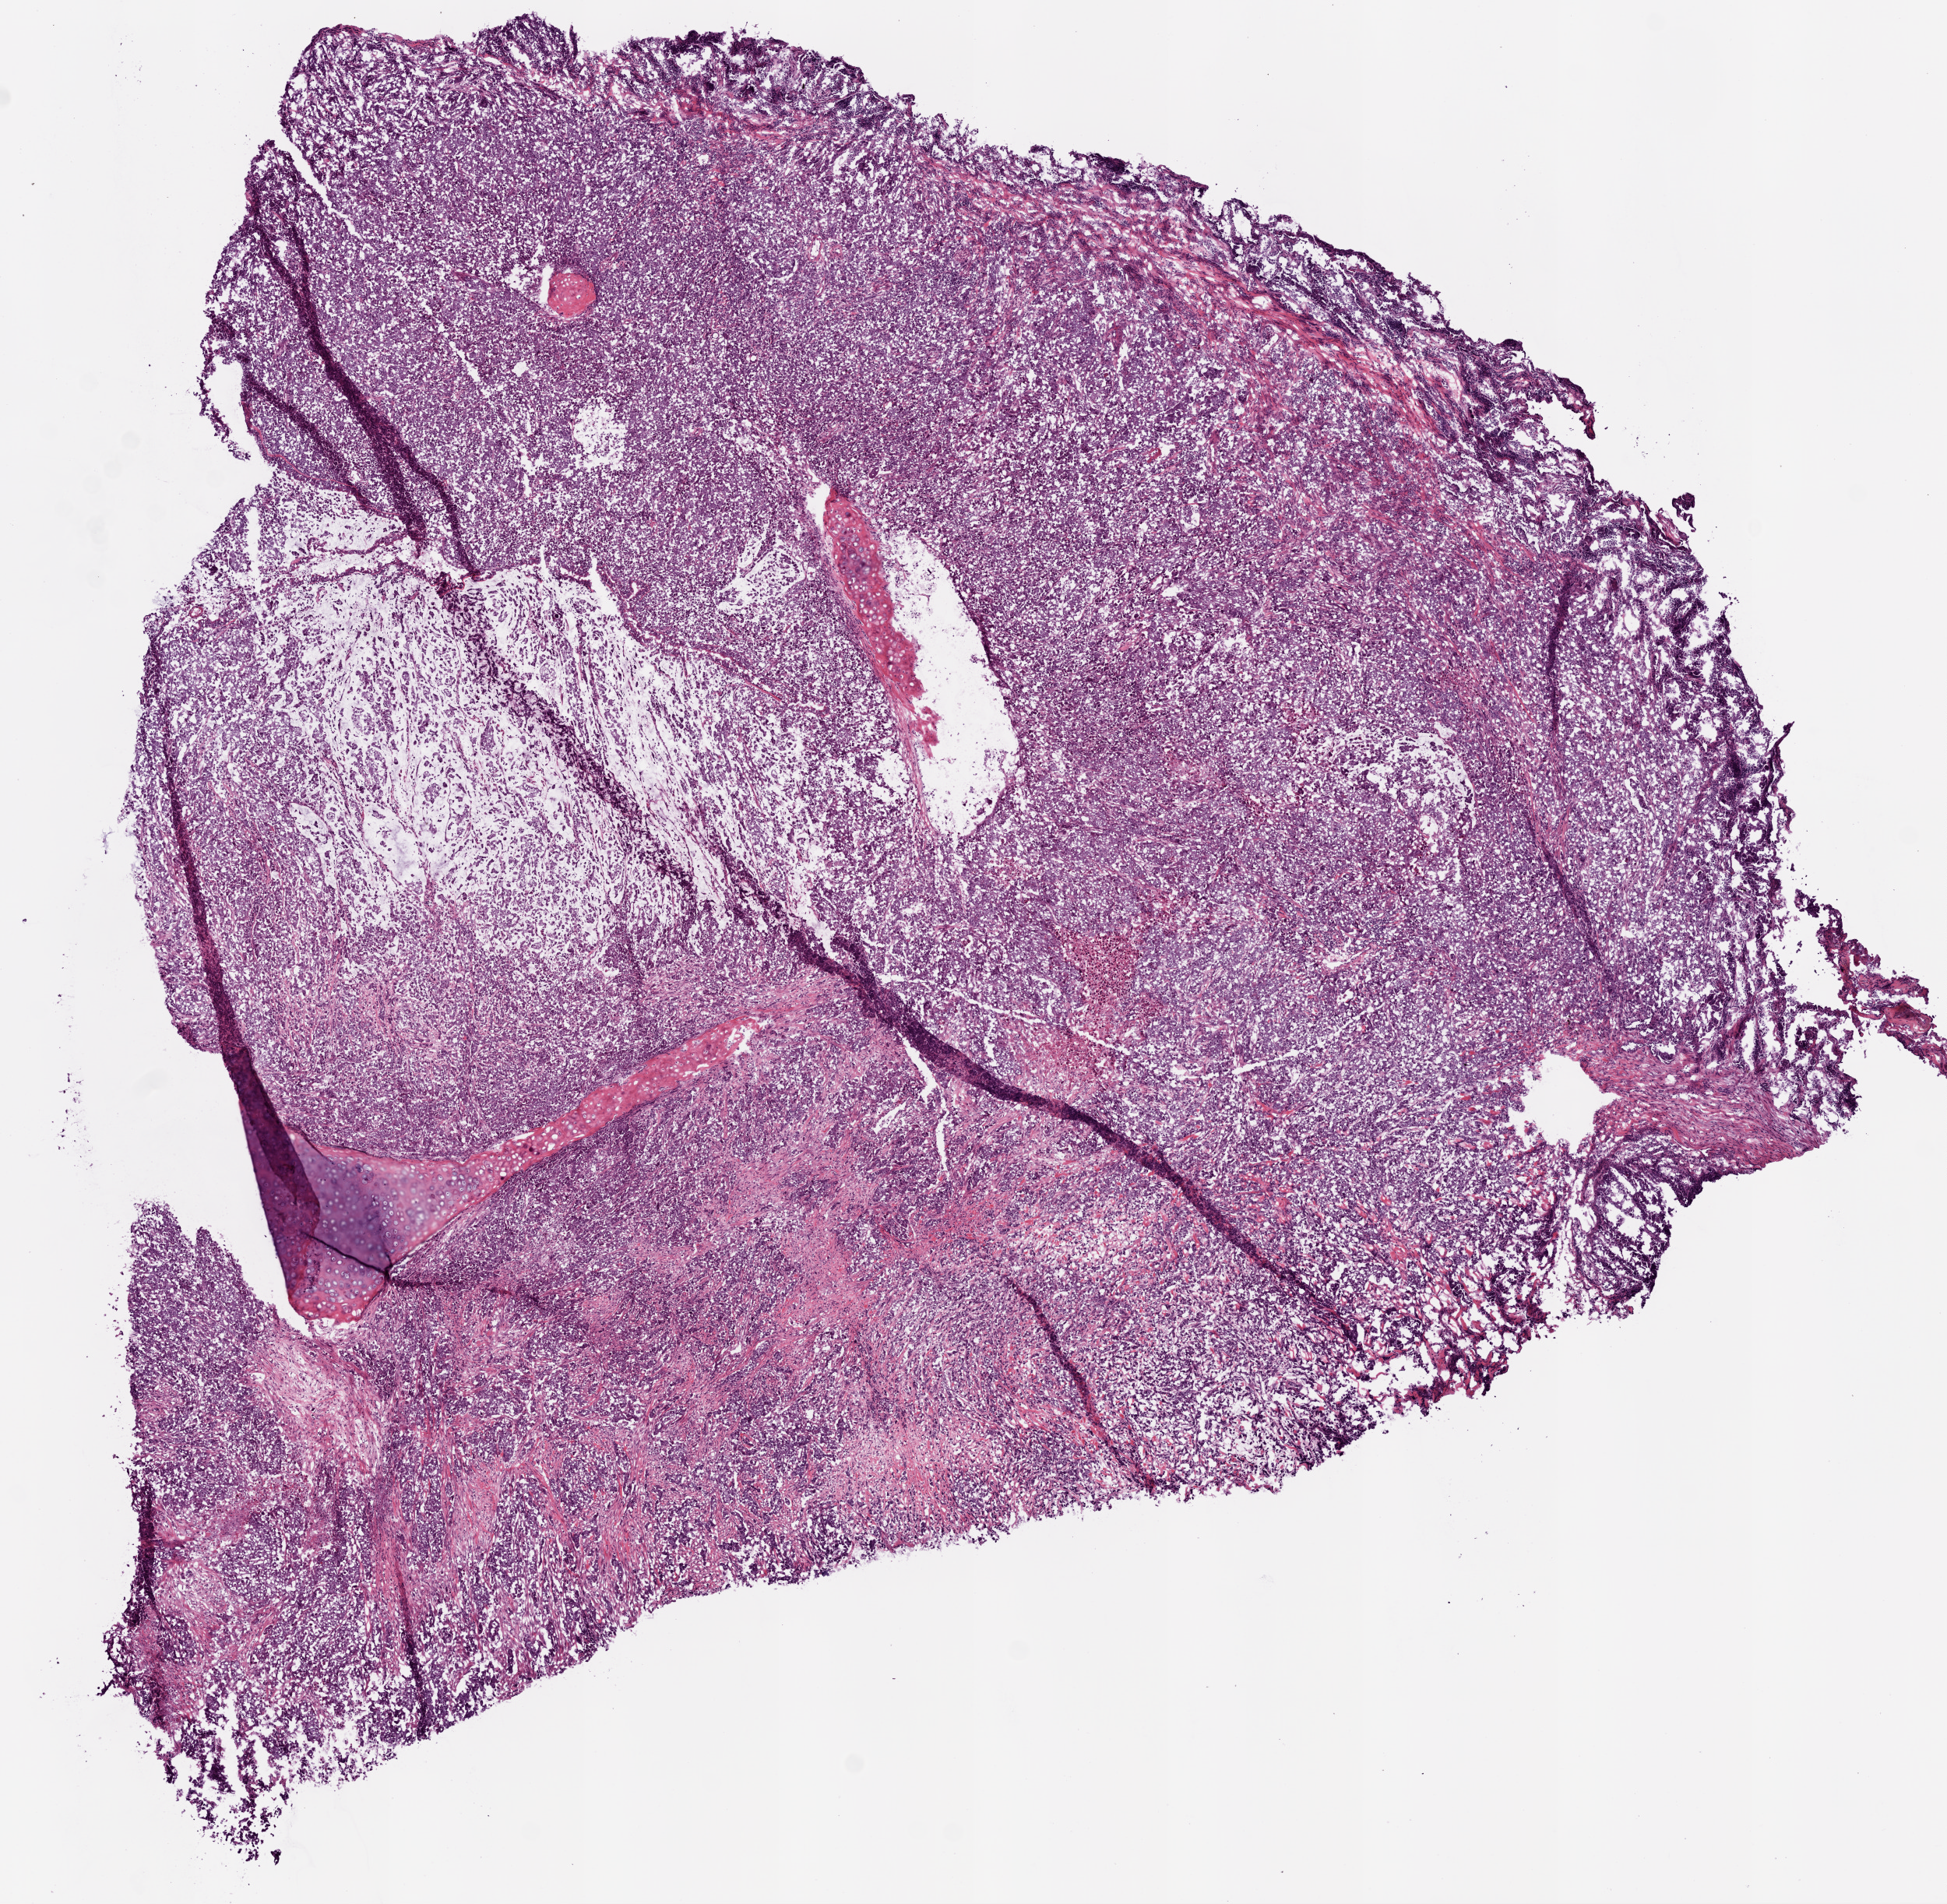
Digitized H&E-stained tissue section (whole slide) — a low-resolution overview of the entire scanned area, about 10.0 x 9.8 mm (acquisition: 20x scan); frozen section from the bottom of the tissue portion; sample: primary tumour, lung. Male, age 65 years at initial diagnosis. Pathologist review of this section (percent, as recorded): tumour cells 90%, tumour nuclei 70%, normal cells 5%, stromal cells 0%, necrosis 5%. Inflammatory infiltration, as recorded: lymphocyte infiltration 10%, monocyte infiltration 2%, neutrophil infiltration 10%.
• AJCC pathologic stage: IIIA
• histologic diagnosis: Squamous cell carcinoma, NOS